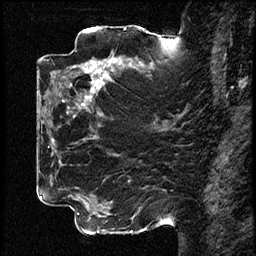
Breast MRI (dynamic contrast-enhanced), one sagittal slice. Slice 37 of 78 in the series (ordered by position). Dynamic contrast-enhanced study with each time point stored as its own series, time point 2 of 3 at this slice position (early post-contrast, ordered by acquisition time). 1.5 T. TE 4.2 ms, TR 17.6 ms. 2 mm slice thickness. 256 × 256 image matrix. Patient: female, 42 years. From the clinical record (not read from this slice): setting: breast cancer imaged before/during neoadjuvant chemotherapy; receptor status: HER2-positive.
Annotated regions visible in this slice (semi-automatic segmentation, software-assisted and operator-edited):
- analysis volume of interest (the breast-tissue region the enhancement analysis was run in; not a lesion): box from (x=50, y=48) to (x=131, y=129) px
- tumour enhancement mask (voxels above the 100 % enhancement threshold inside the analysis volume of interest): (x=74, y=59)–(x=118, y=117)